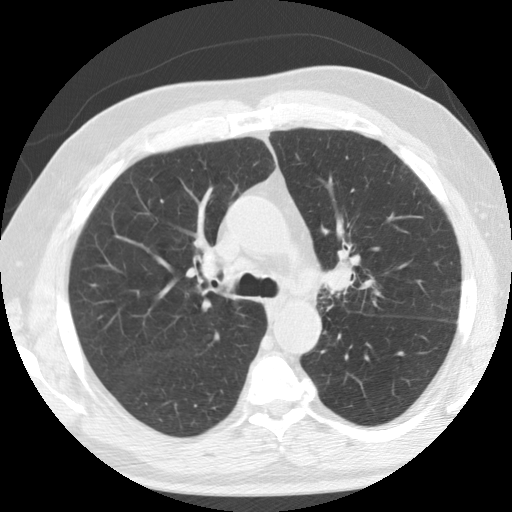
Low-dose screening chest CT, axial slice, second annual screen, lung window (W 1500 / L -600 HU), 2.5 mm slice thickness, 120 kVp, slice 46 of 133 in the series, 512 × 512 image matrix, field of view 342 × 342 mm. Male participant, aged 74 years at enrolment.
Lesion marked by an expert reader, bounding box (x1, y1, x2, y2) in pixels: (303, 251, 369, 317). No non-calcified nodule or mass ≥4 mm was recorded by the screening reader at this exam. Official screen result: positive, other. Lung cancer was diagnosed 274 days after this screen: non-small cell carcinoma, left upper lobe, poorly differentiated (G3), stage IIB (AJCC 6th edition).